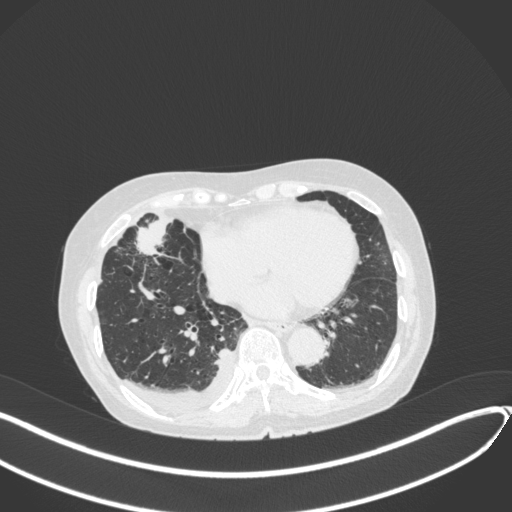
Chest CT, one axial slice. Slice 132 of 418 in the series (ordered by position). Lung window (W 1500 / L -600 HU). 1 mm slice thickness. 512 × 512 image matrix. Patient: female, 75 years. From the clinical record (not read from this slice): clinical TNM (as recorded): T2a N3 M0.
Annotated regions visible in this slice (rectangle marked by the reading radiologist):
- lung tumour (recorded histology: adenocarcinoma): bounding box <133,204,174,256> (left, top, right, bottom; pixels)